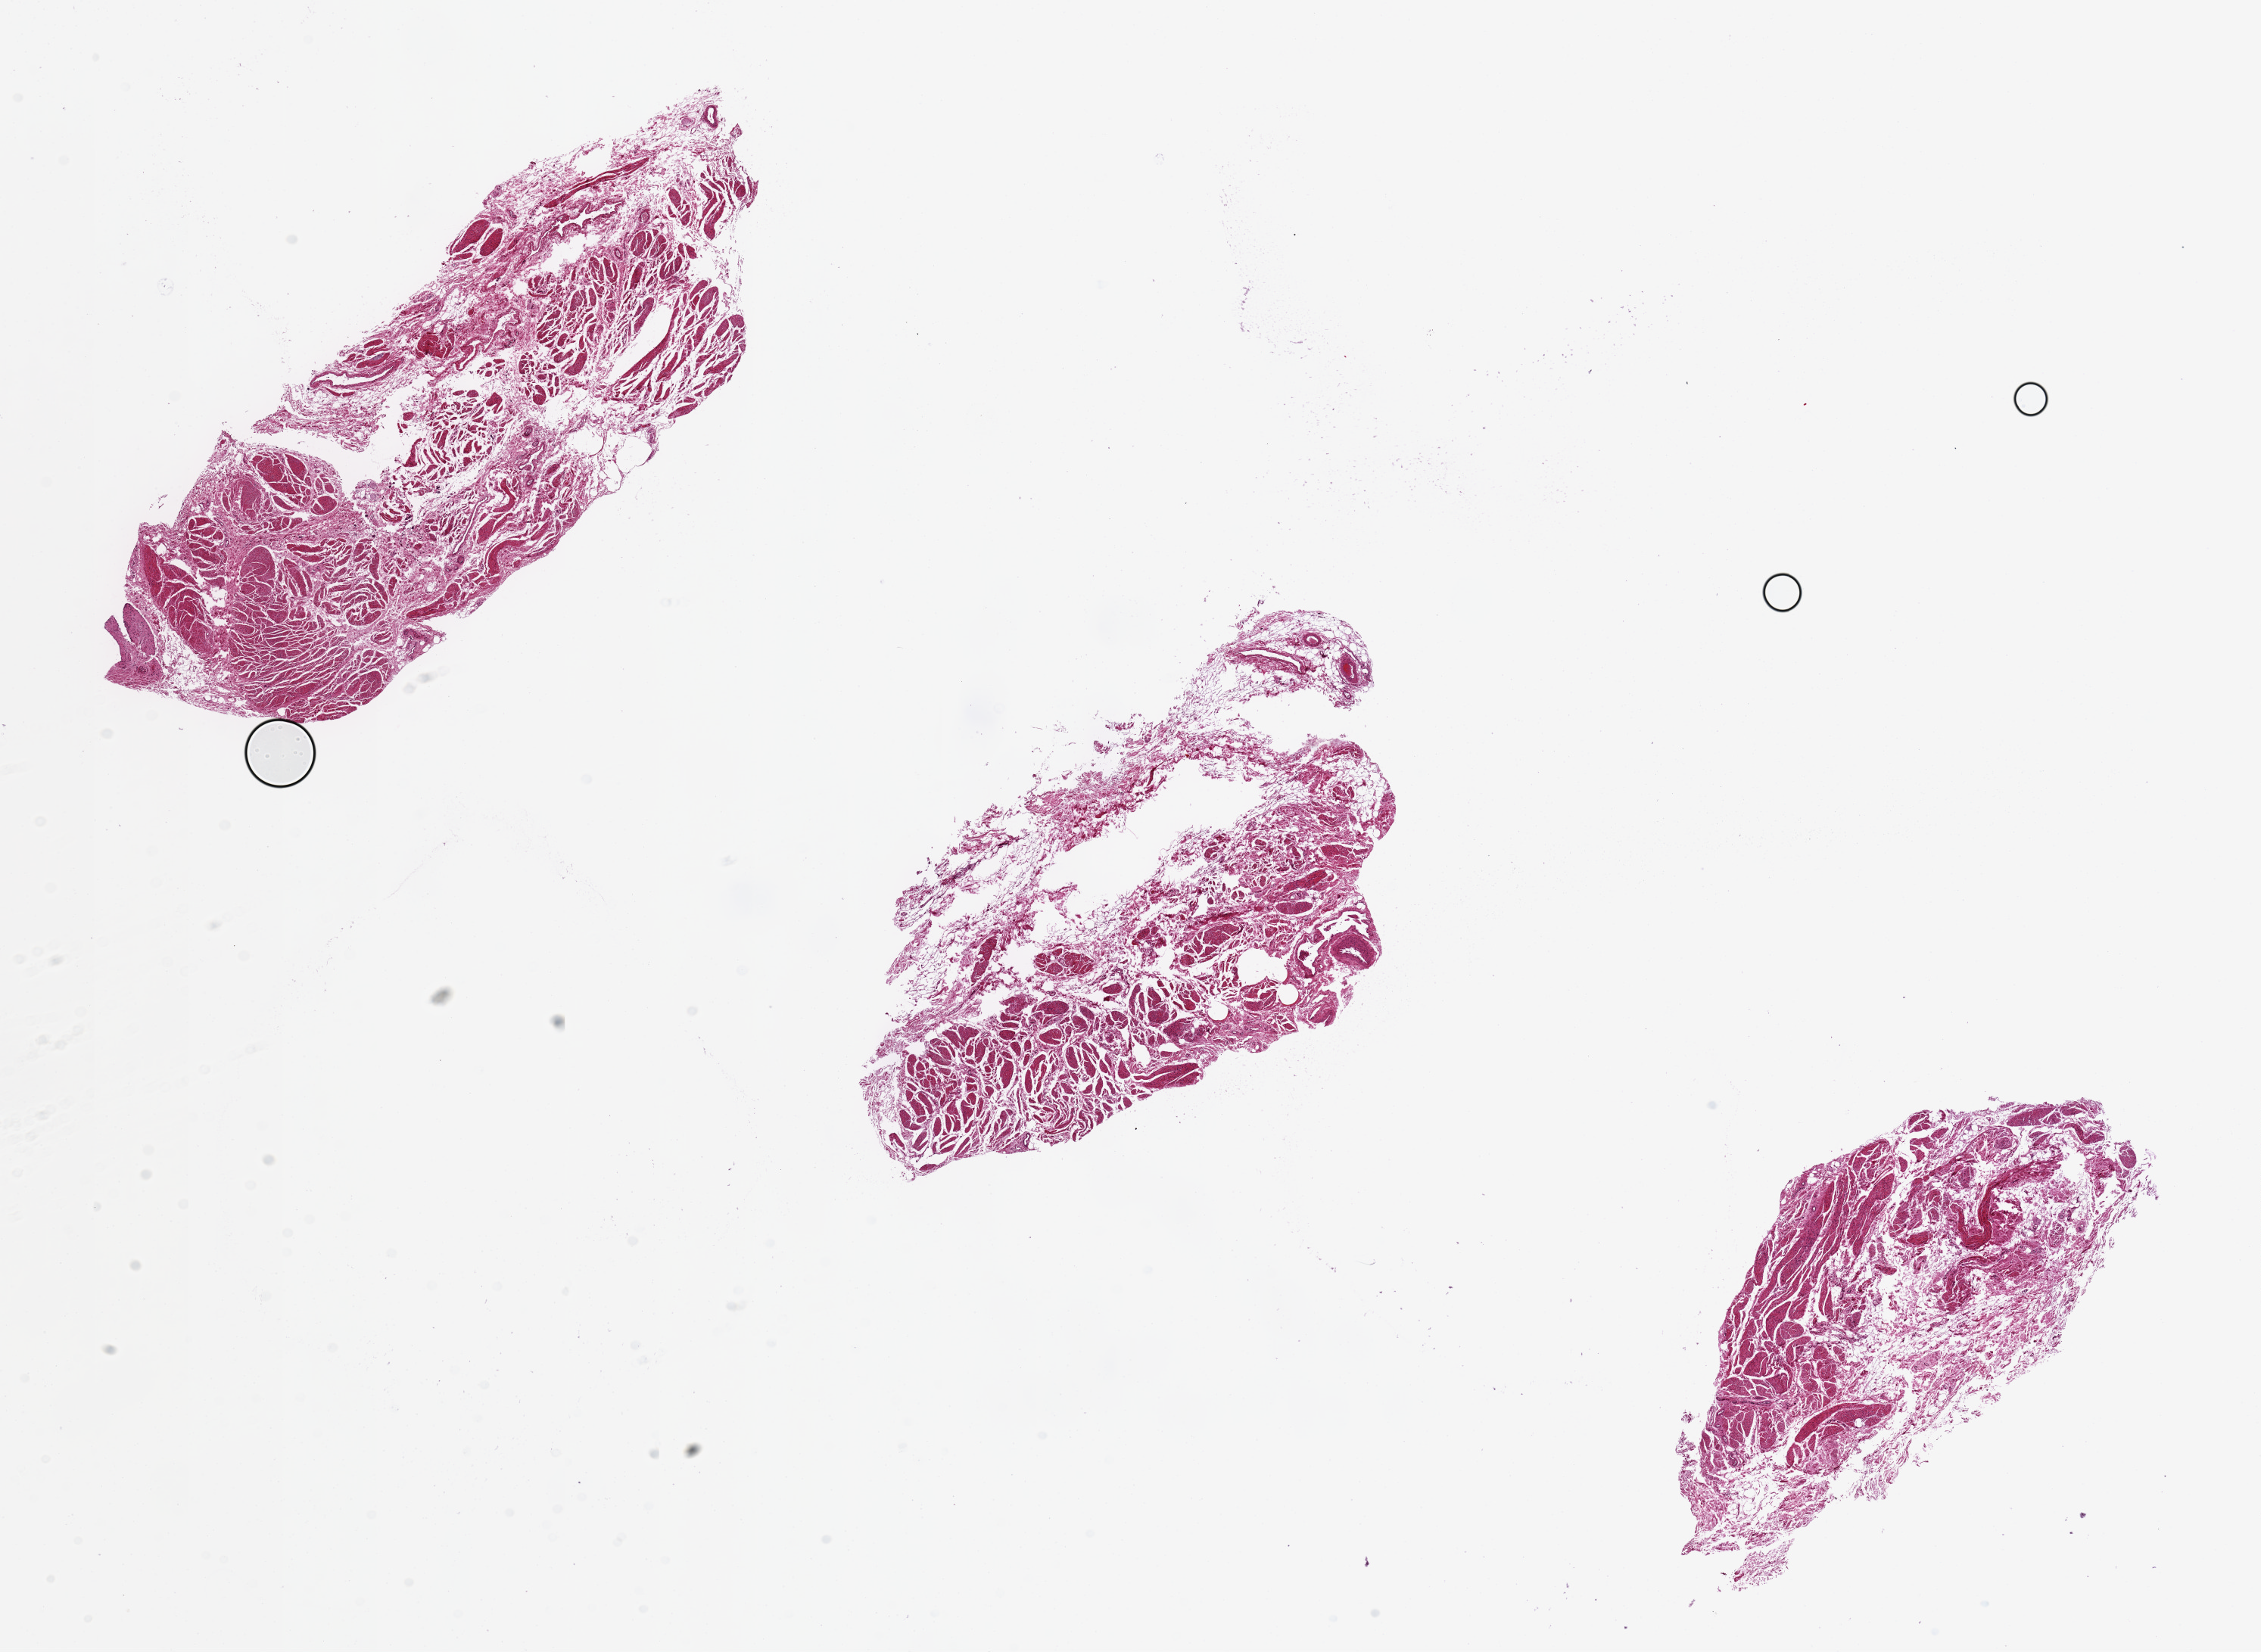
Digitized H&E-stained section, brightfield — a low-resolution overview of the entire scanned area, about 23.6 x 17.3 mm (from a 20x scan); PAXgene-fixed, paraffin-embedded tissue; section of urinary bladder (target tissue); tissue donor sample.
Reviewer comment on this tissue sample: 3 ~8x3mm pieces. Mucosa completely sloughed. Poorly fixed muscle, many holes/tears.